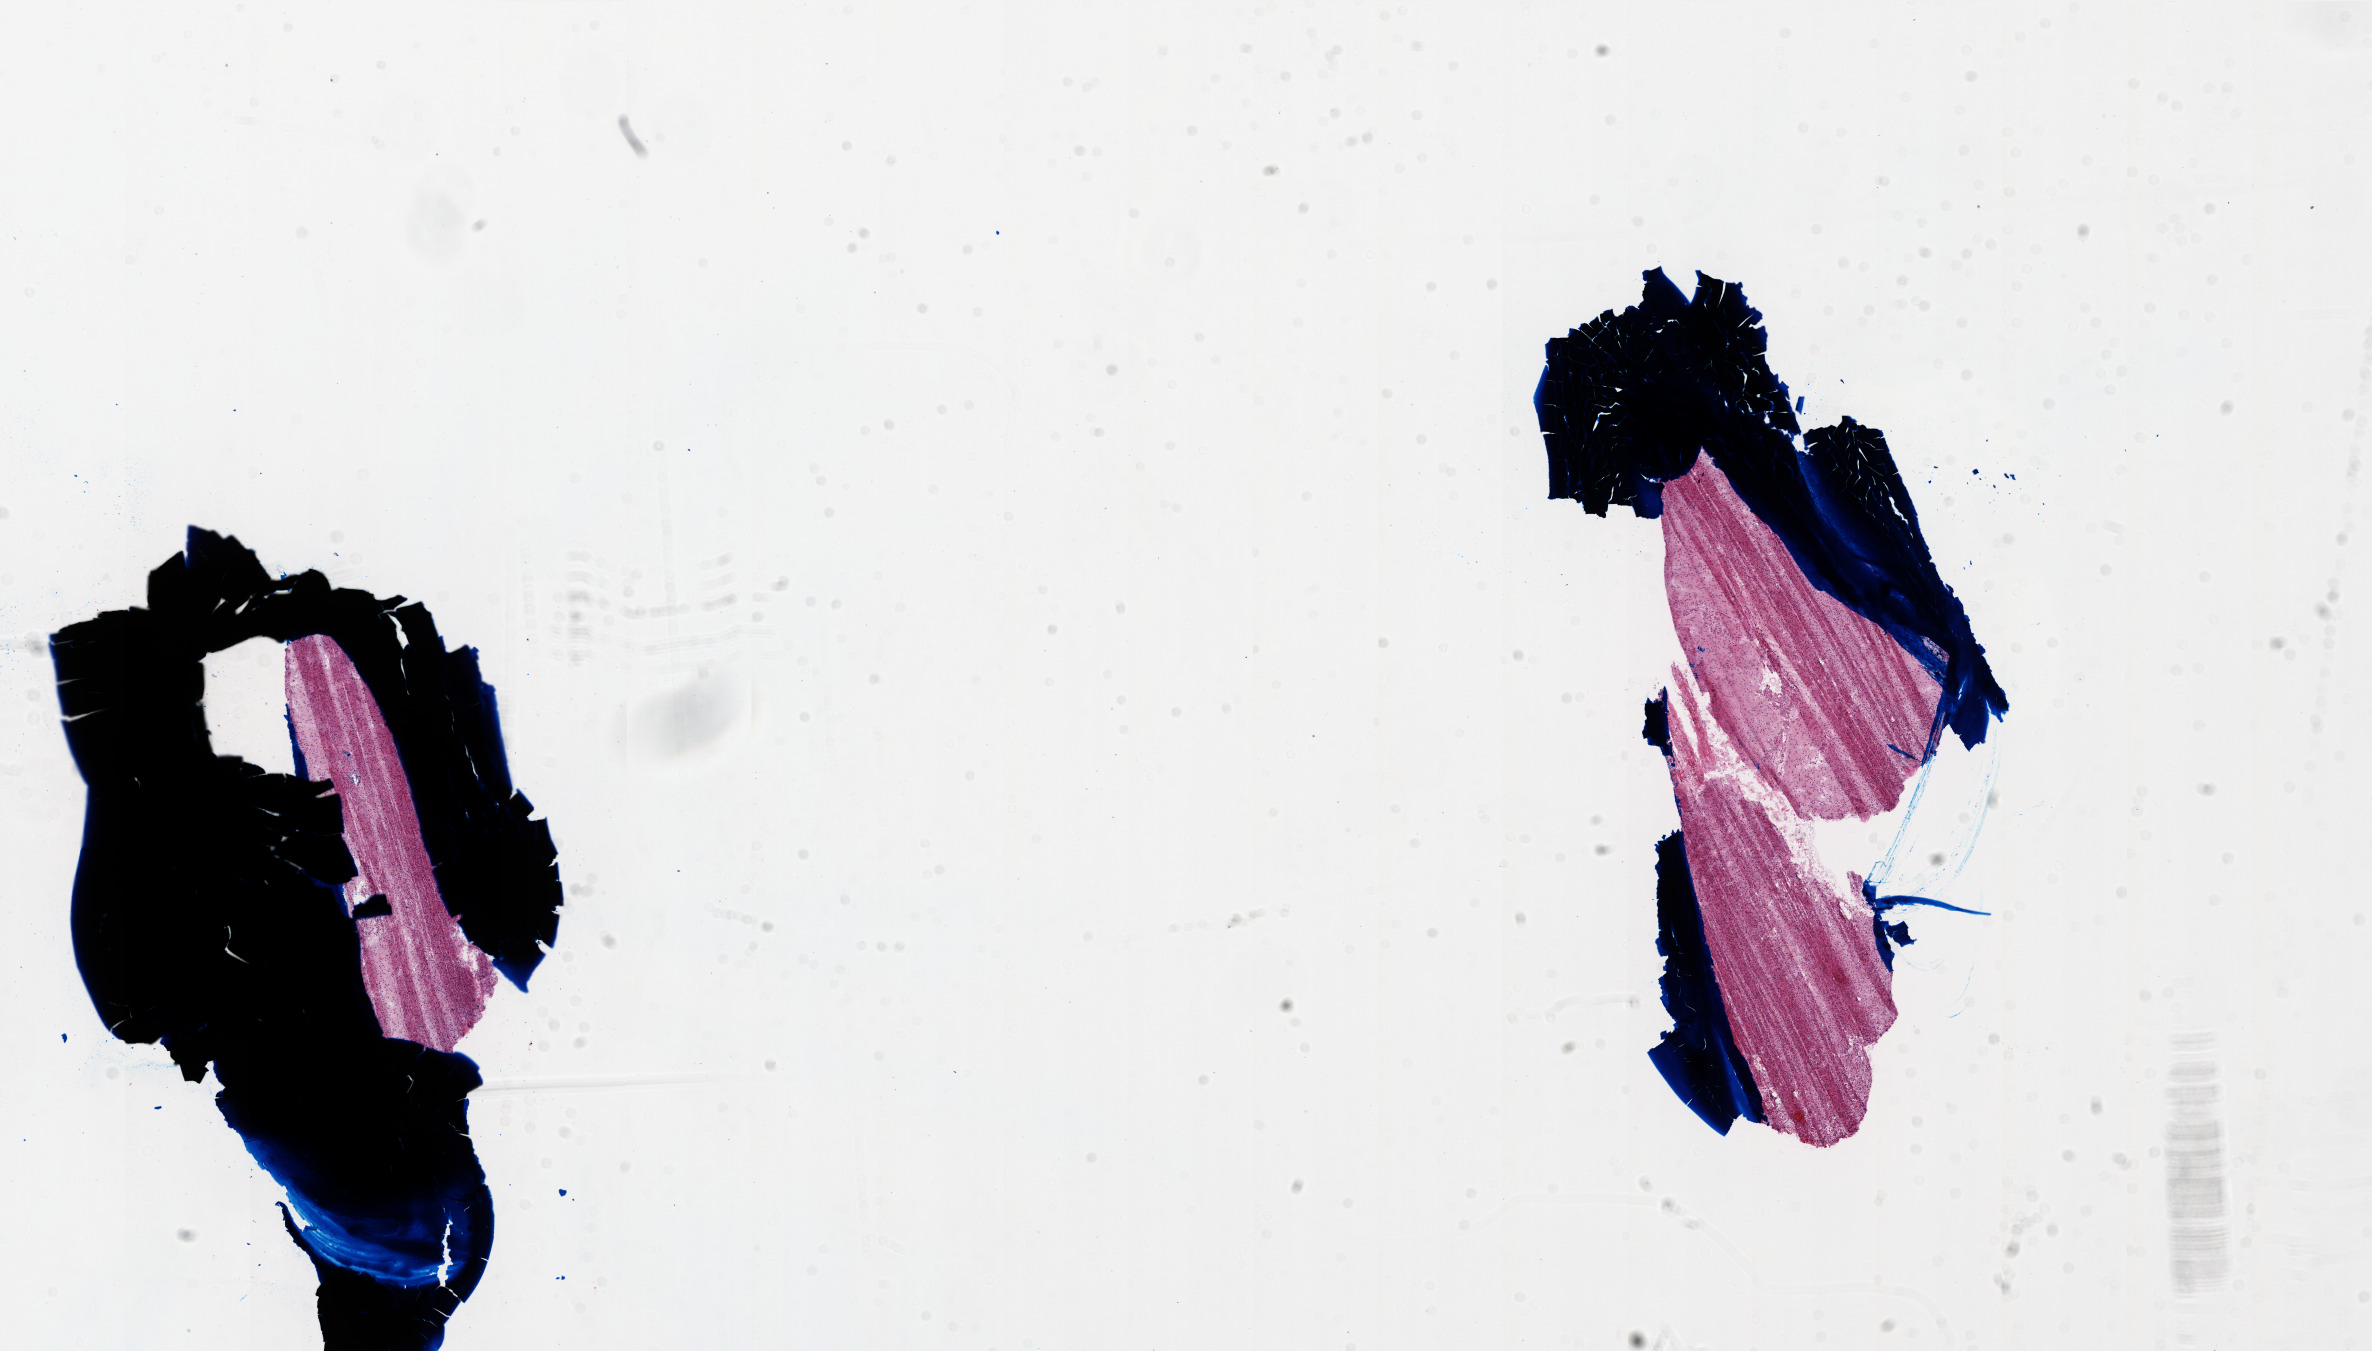
Digitized Hematoxylin and eosin (H&E) stained tissue section (whole slide) — low-resolution overview of the scanned area, about 19.0 x 10.8 mm (acquisition: 20x scan), frozen section from the top of the tissue portion, brain, primary tumour sample. Female, age 63 years at initial diagnosis.
Histologic diagnosis: Glioblastoma.